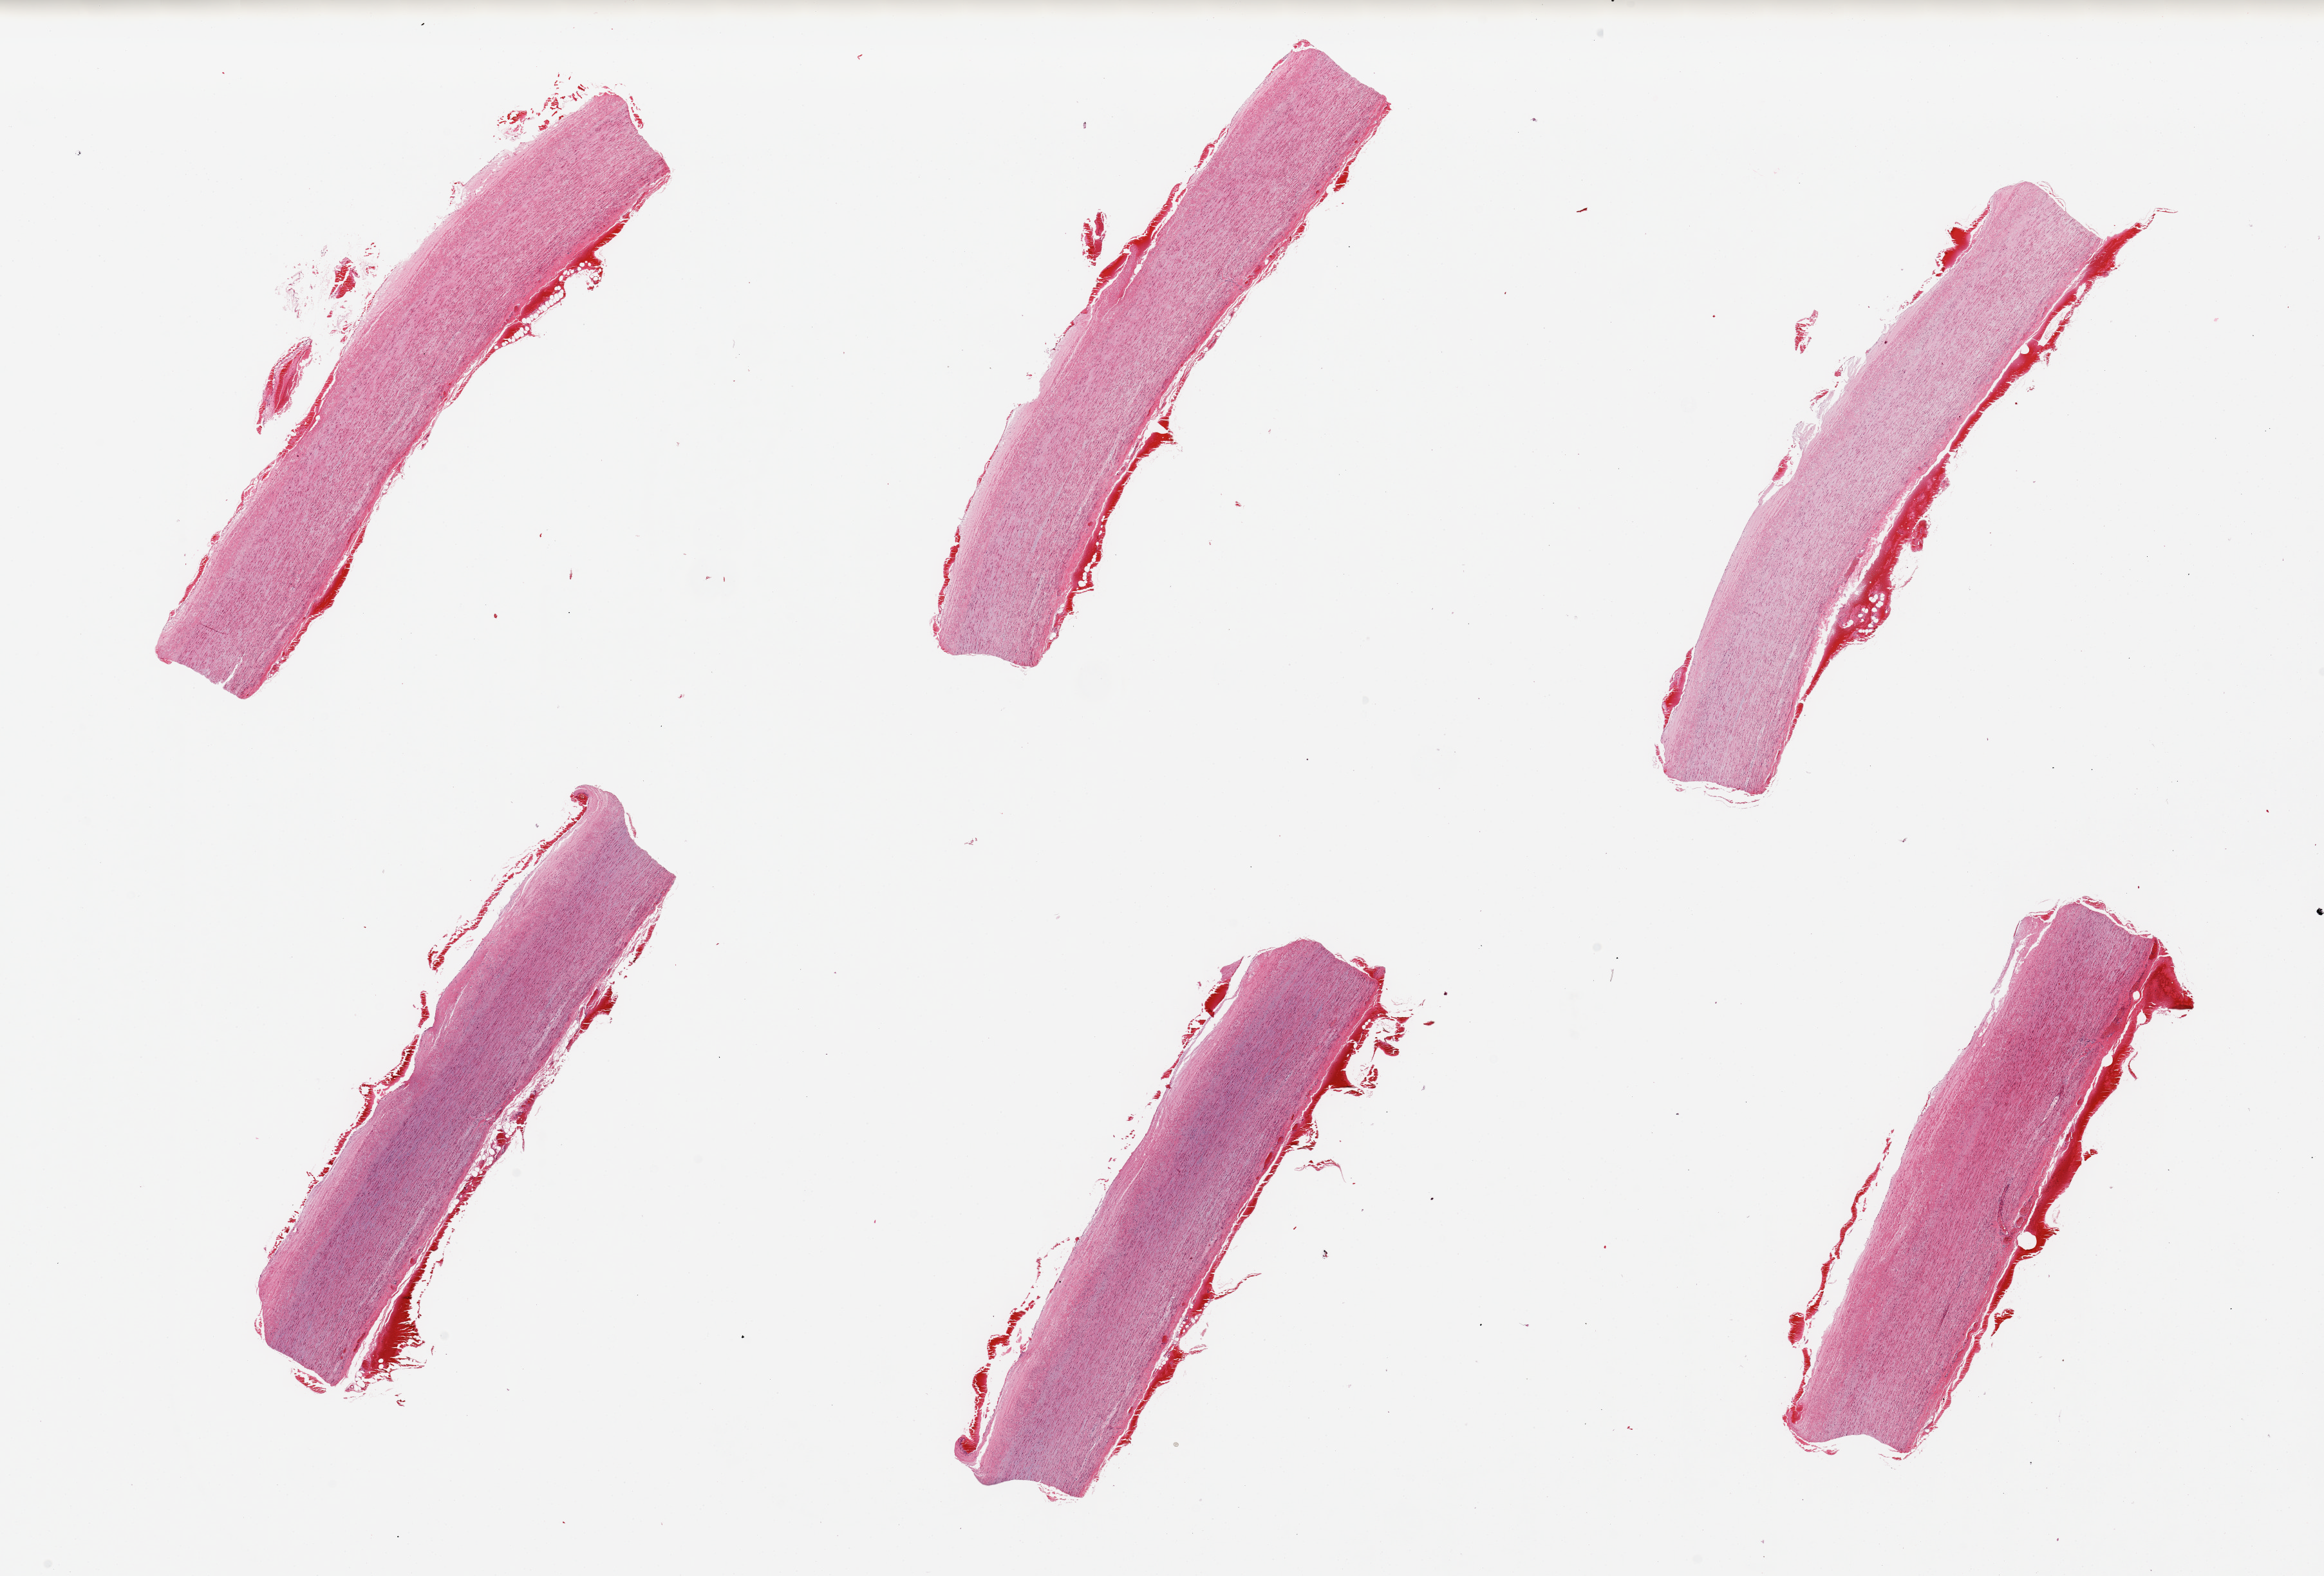
Whole-slide image, haematoxylin and eosin stain, shown as a low-resolution overview of the whole scanned area (about 28.5 x 19.4 mm, acquisition: 20x scan), PAXgene-fixed, paraffin-embedded tissue, section of aorta (target tissue), donor tissue sample. Male donor.
* pathologist's review note for this sample: 6 pieces; well trimmed